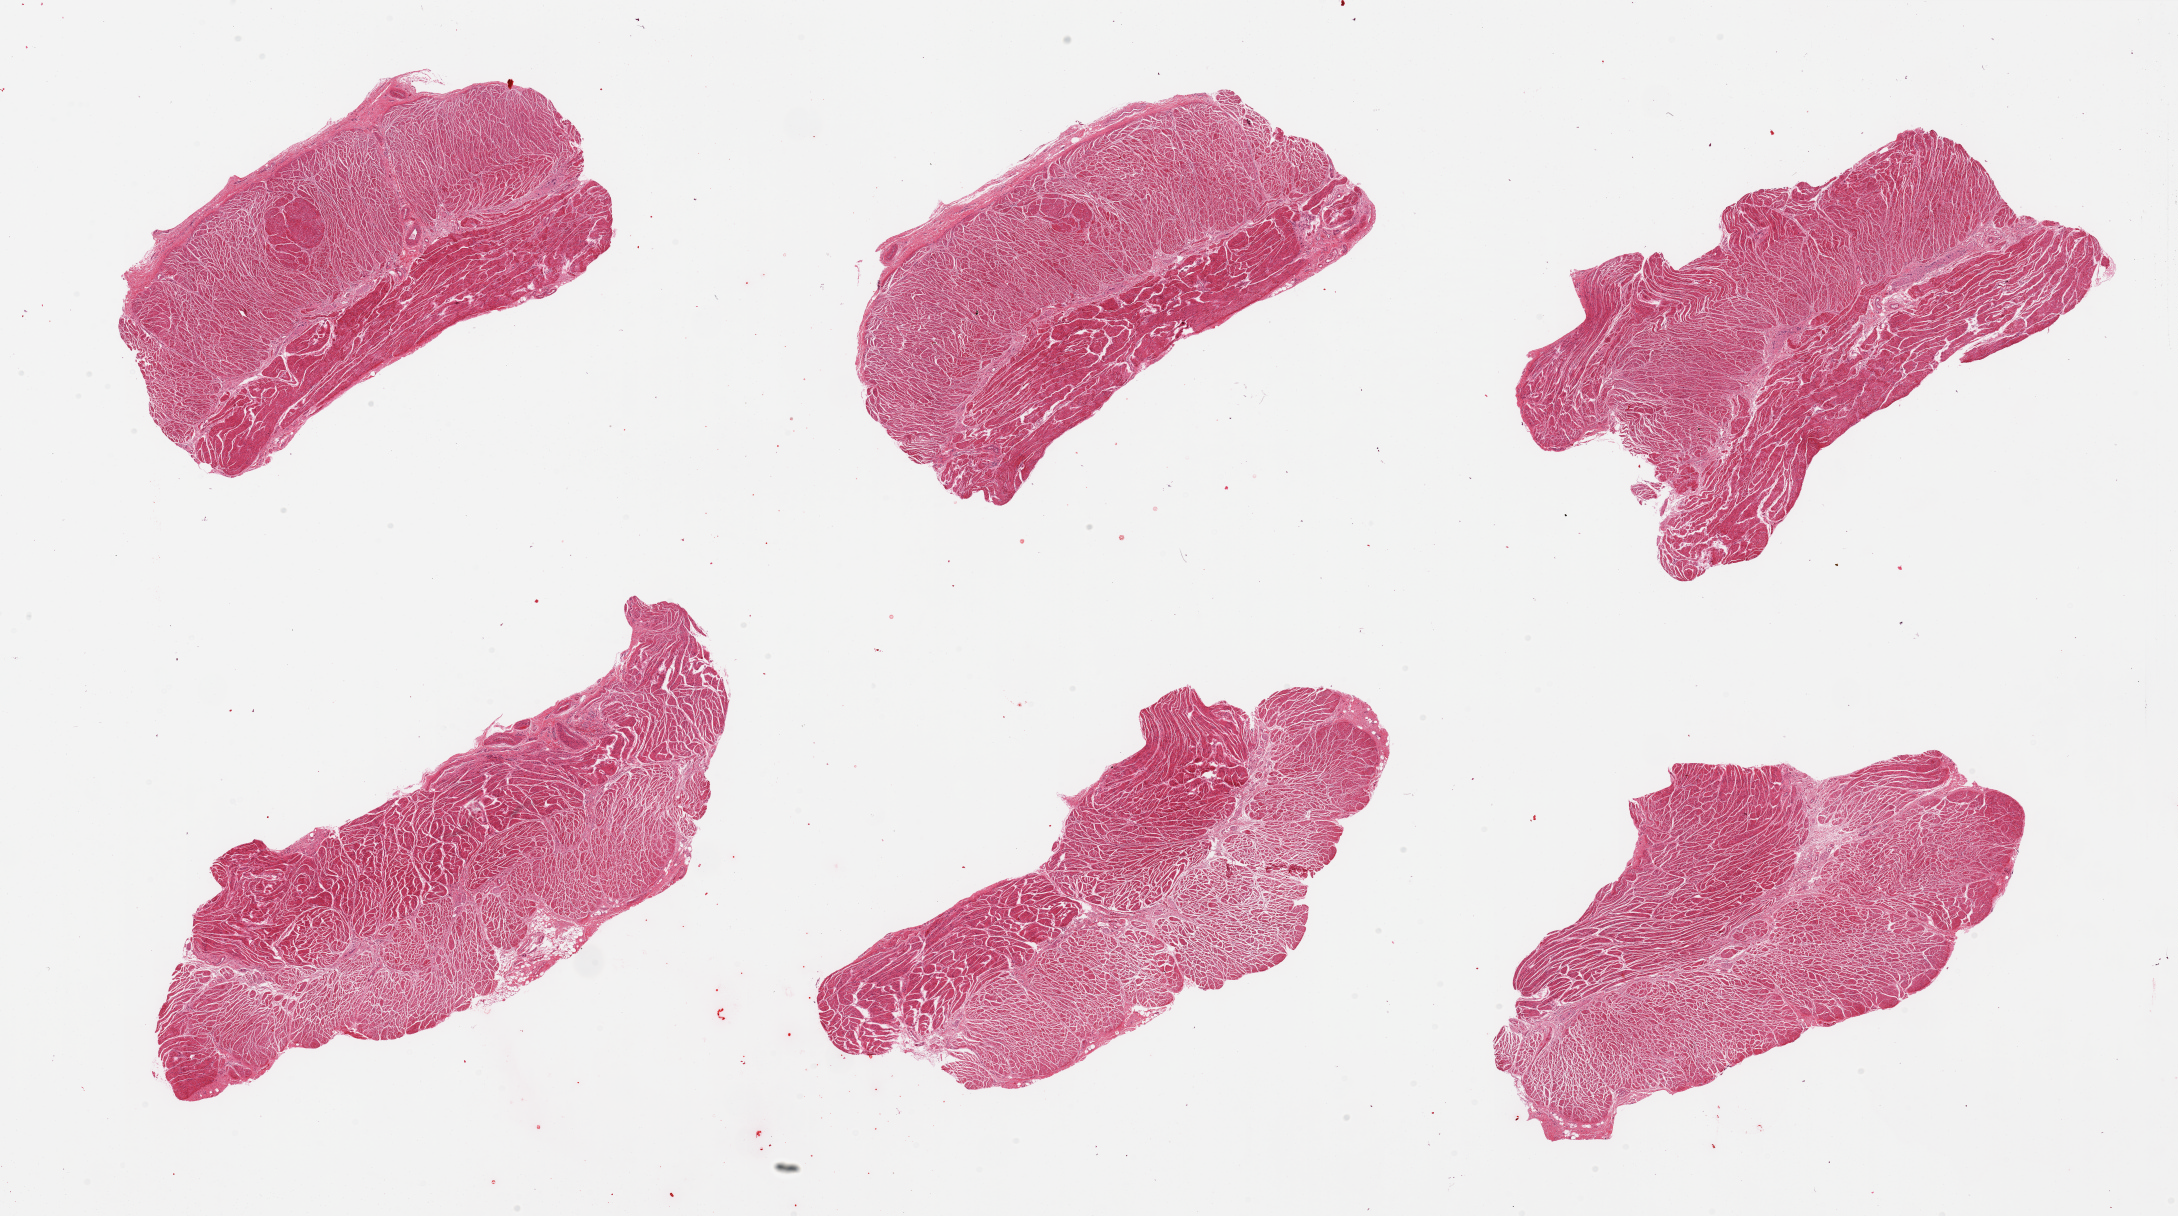
Whole-slide image, H&E stain, brightfield — a low-resolution overview of the entire scanned area, about 34.5 x 19.2 mm, PAXgene-fixed paraffin-embedded (PFPE) section, sampled site (target tissue): esophageal muscle, tissue donor sample. Donor sex: female.
Reviewer comment on this tissue sample: 6 pieces, well trimmed.